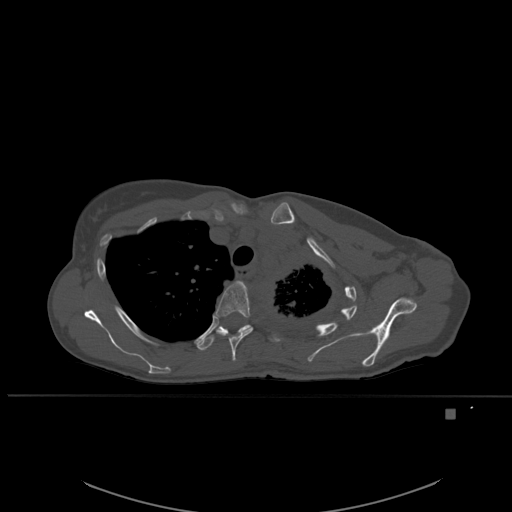
CT including the spine, one axial slice. Position 409 of 537 along the scan axis. Bone window (W 1800 / L 400 HU). 1.5 mm slice thickness. 512 × 512 image matrix, field of view 440 × 440 mm. Patient: female, 45 years. Case-level facts recorded for this patient, not image findings: primary cancer: lung.
Outlined on this slice (semi-automatically segmented with operator editing):
- T4 vertebra: bounding box (x1, y1, x2, y2) in pixels: (216, 281, 253, 362)
- T5 vertebra: (196, 321, 251, 351)